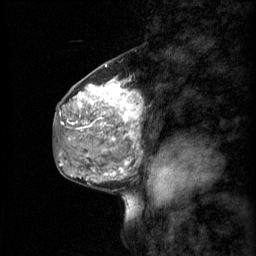
Breast MRI (dynamic contrast-enhanced), one sagittal slice; slice 30 of 60 in the series (ordered by position); 3 images stored at this slice position (order not interpretable as contrast timing); 1.5 T; TE 4.2 ms, TR 11 ms; 2 mm slice thickness; 256 × 256 image matrix. Female patient, age 48 years.
Outlined on this slice (semi-automatic segmentation, software-assisted and operator-edited):
- analysis volume of interest (the breast-tissue region the enhancement analysis was run in; not a lesion): box from (x=69, y=74) to (x=140, y=147) px
- tumour enhancement mask (voxels above the 70 % enhancement threshold inside the analysis volume of interest): (x=74, y=76)–(x=140, y=147)